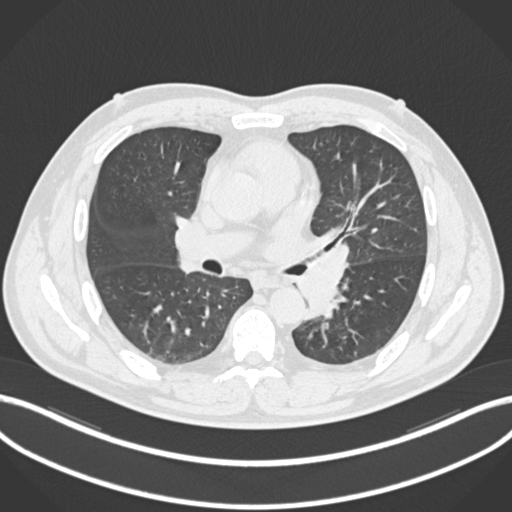
Chest CT, one axial slice. Position 125 of 223 along the scan axis. Lung window (W 1500 / L -600 HU). 512 × 512 image matrix, field of view 400 × 400 mm. Male patient, age 50 years. Case-level facts recorded for this patient, not image findings: clinical TNM (as recorded): T2a N3 M0.
Annotated regions visible in this slice (rectangle marked by the reading radiologist):
- lung tumour (recorded histology: squamous cell carcinoma): box from (x=294, y=238) to (x=351, y=313) px